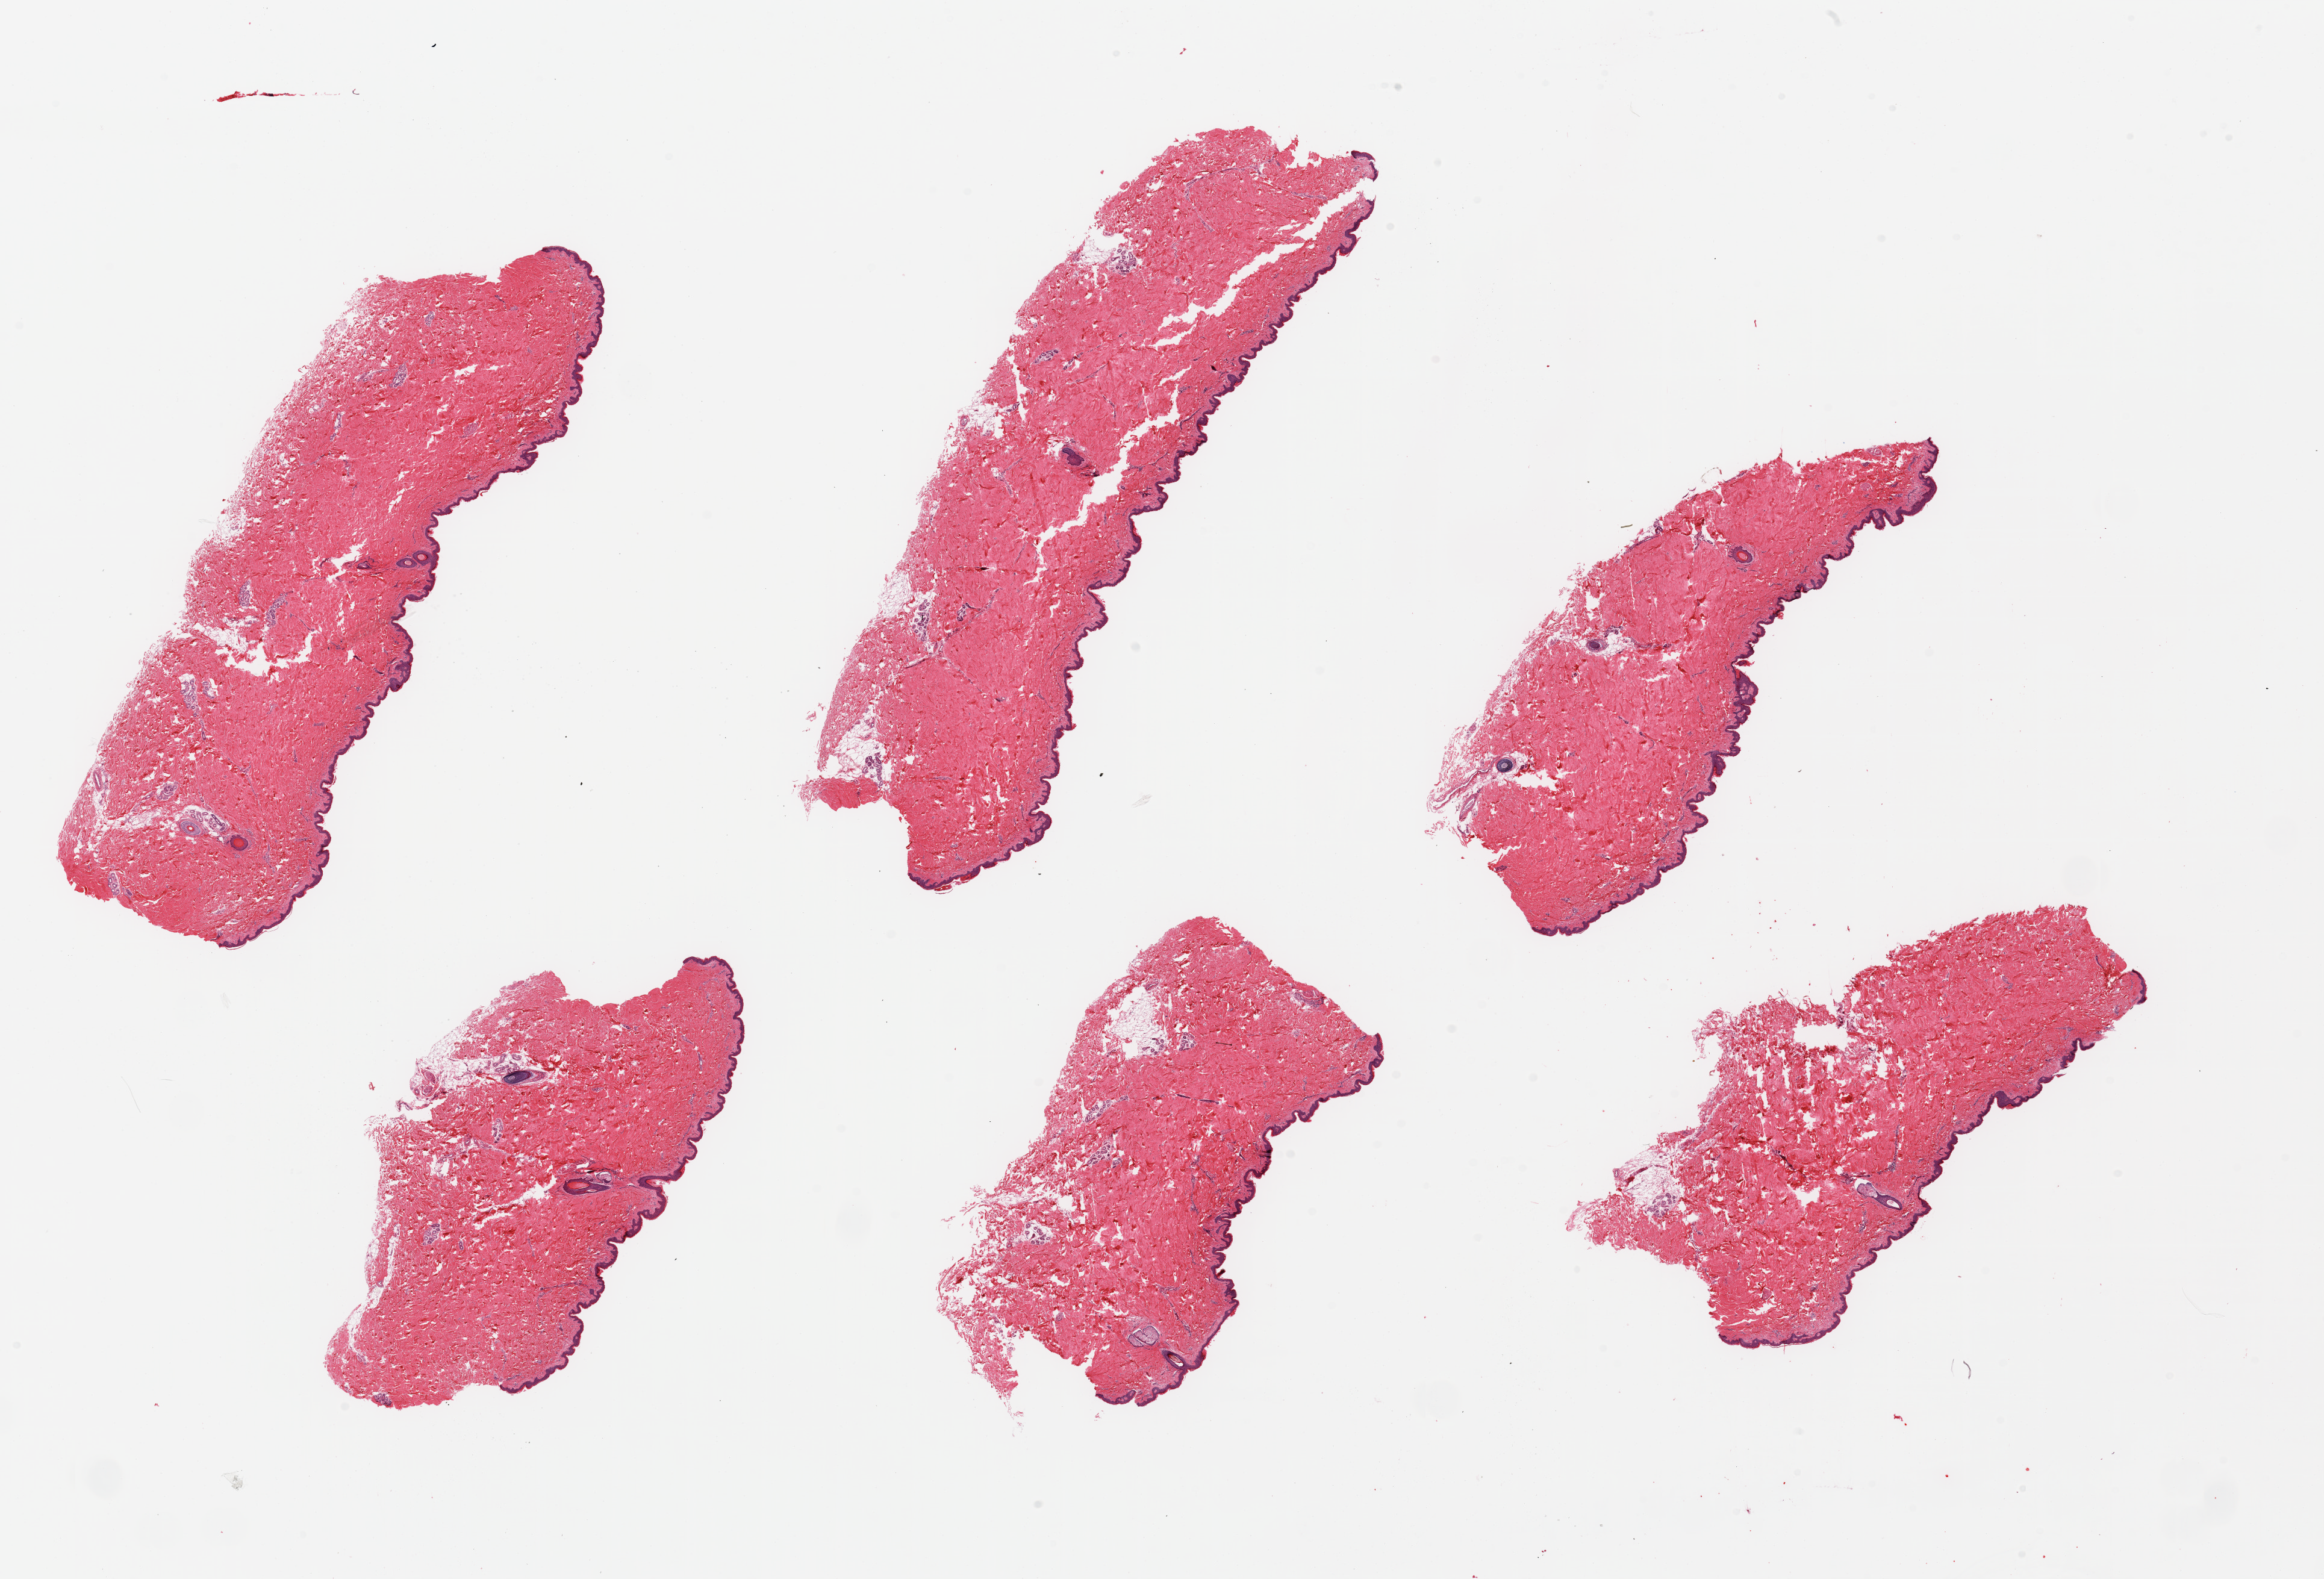
Digitized H&E-stained section — low-resolution overview of the scanned area, about 30.5 x 20.7 mm, PAXgene-fixed, paraffin-embedded tissue, section of skin of suprapubic region (target tissue), tissue donor sample. Donor: male.
* pathologist's review note for this sample: 6 pieces; well trimmed, minimal internal fat